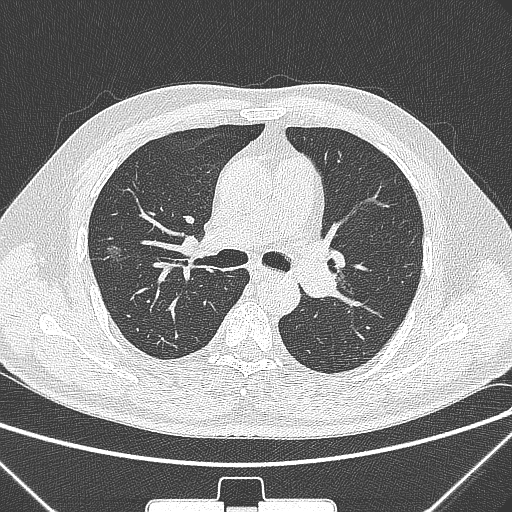
Chest CT, one axial slice. Slice 192 of 320 in the series (ordered by position). Lung window (W 1500 / L -600 HU). 1 mm slice thickness. 512 × 512 image matrix, field of view 350 × 350 mm. Patient: male, 58 years. From the clinical record (not read from this slice): clinical TNM (as recorded): T1c N0 M0.
Annotated regions visible in this slice (rectangle marked by the reading radiologist):
- lung tumour (recorded histology: adenocarcinoma): bounding box [x1, y1, x2, y2] px = [95, 239, 124, 271]